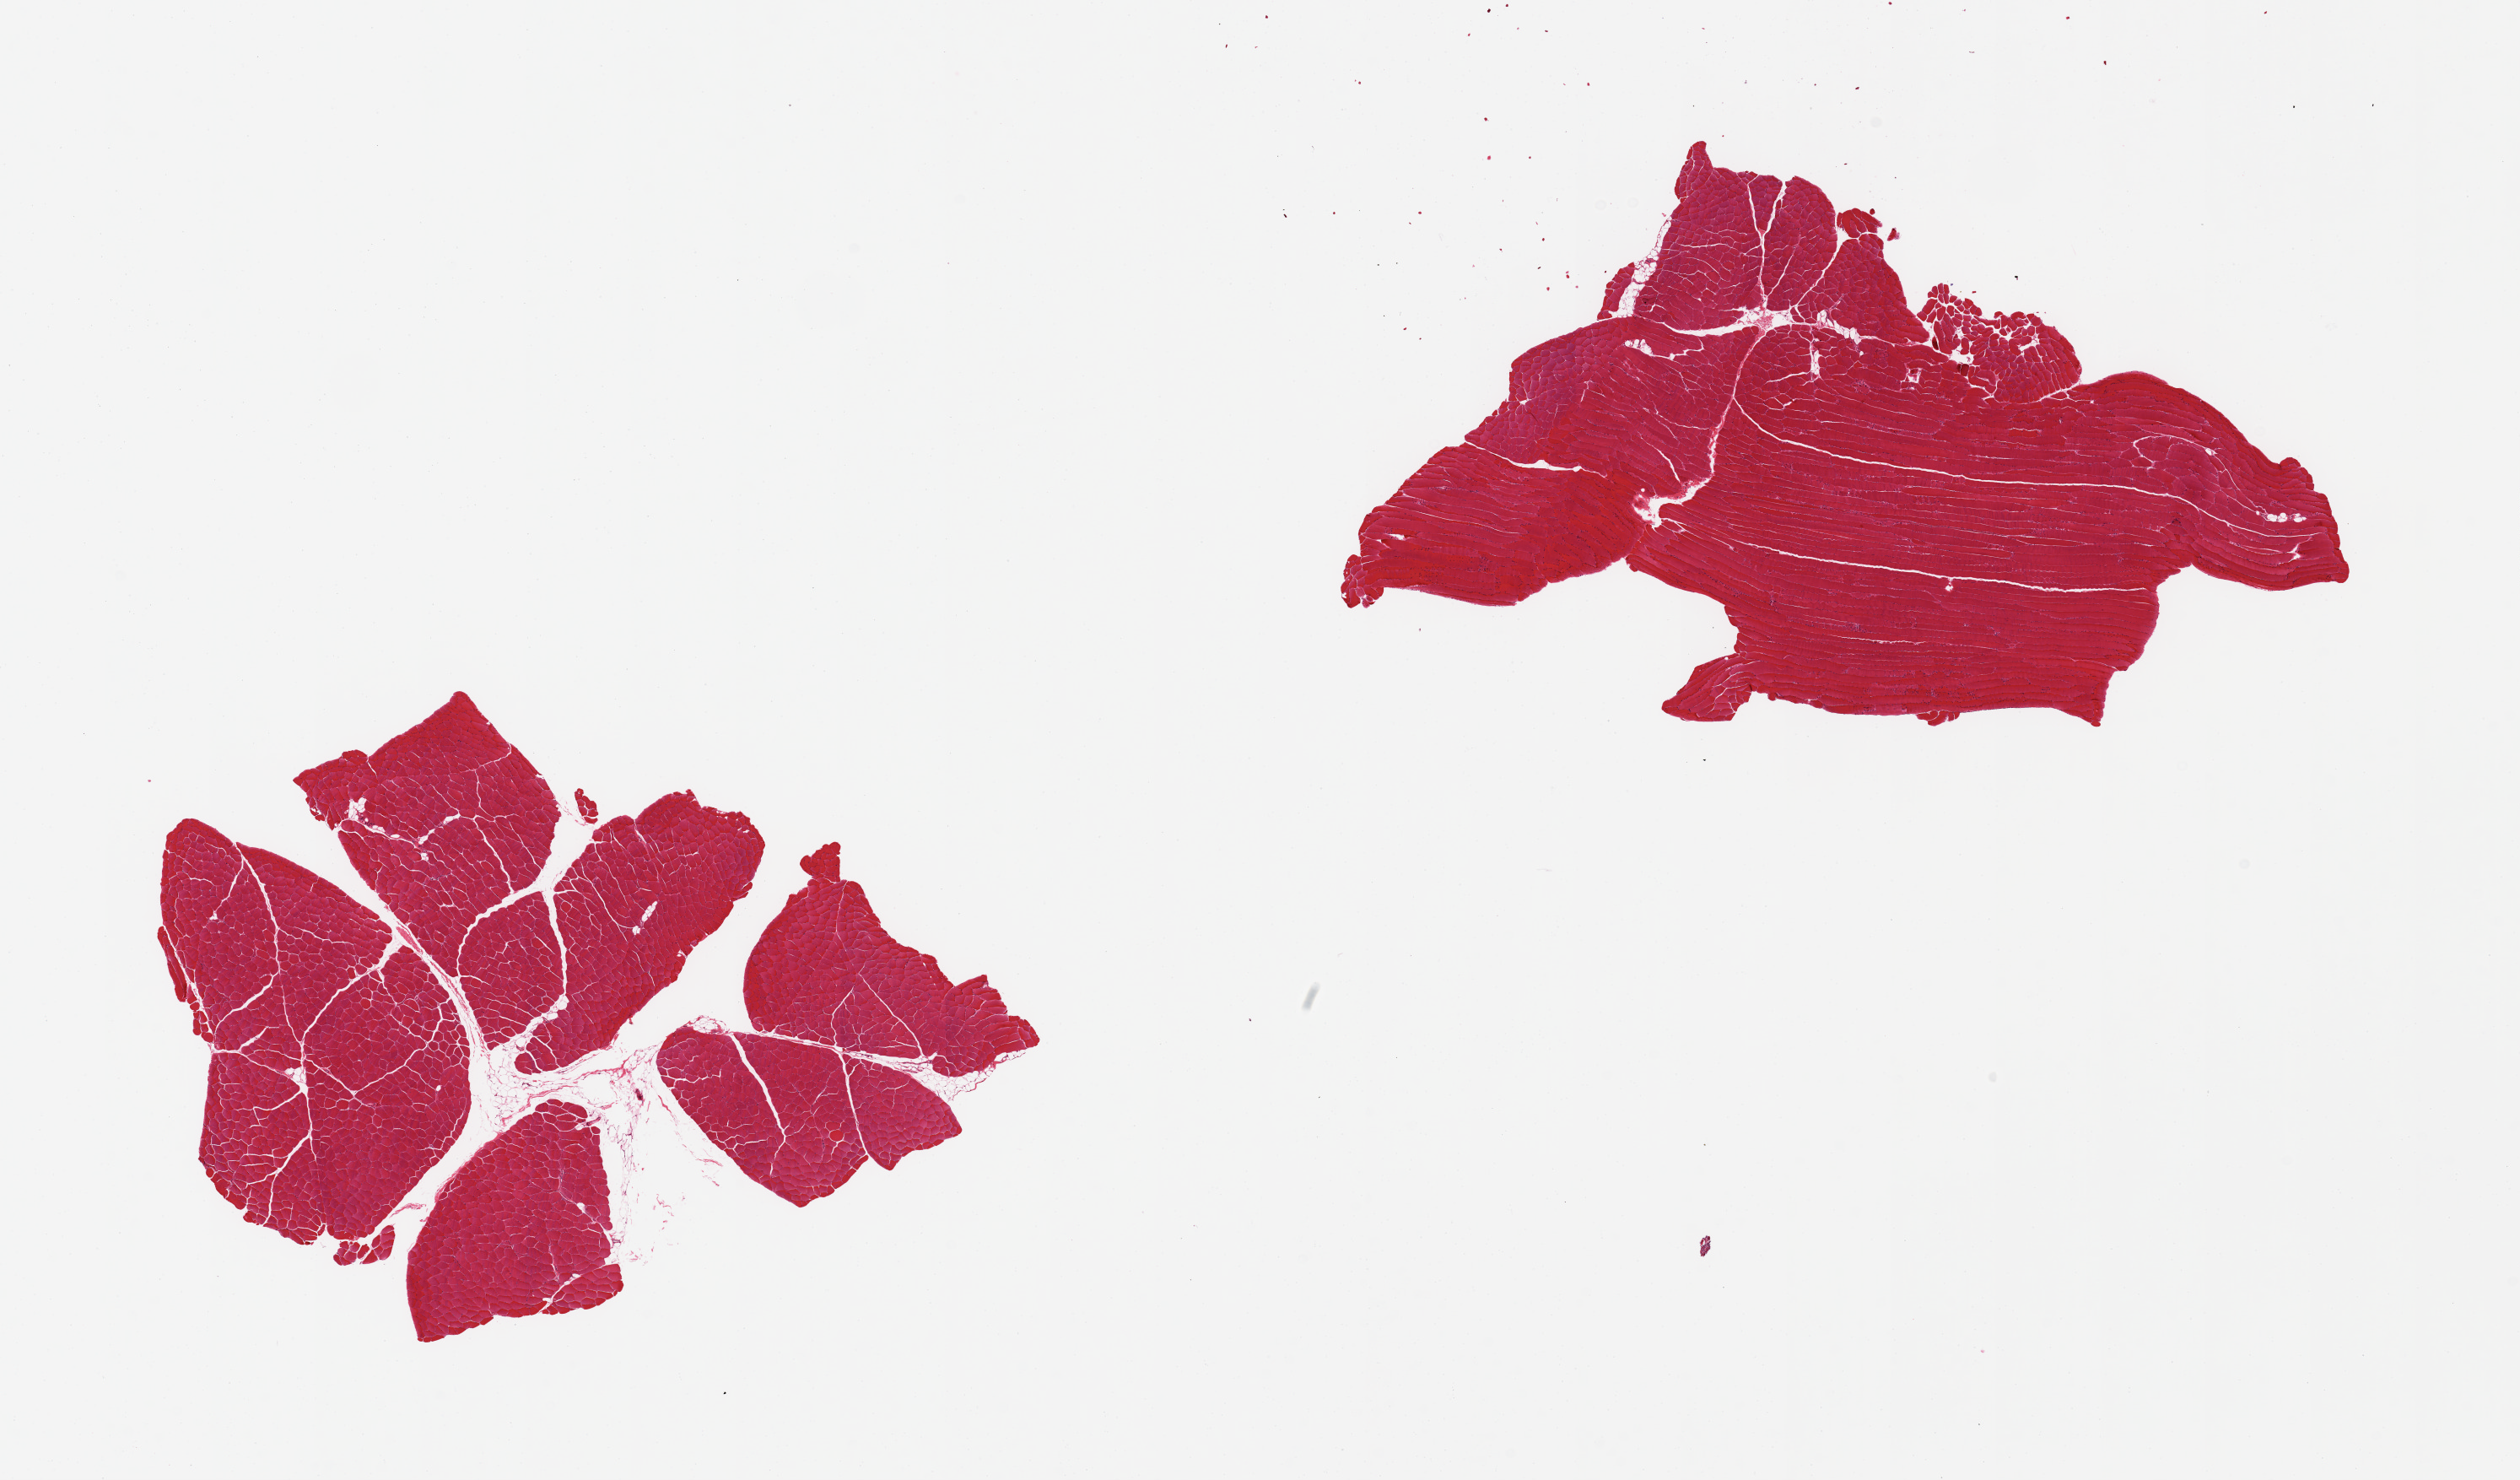
Digitized H&E-stained section, brightfield — shown as a low-resolution overview of the whole scanned area (about 23.6 x 13.9 mm). PAXgene-fixed paraffin-embedded (PFPE) section. Section of skeletal muscle (target tissue). Donor tissue sample. Female donor.
* reviewer comment on this tissue sample: 2 pieces, one piece includes small portion of internal fat